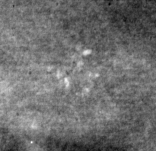
Region of interest cut from a scanned film mammogram (one marked finding); left breast; CC view.
Calcifications, morphology punctate, distribution clustered; BI-RADS assessment category 4; subtlety rating 1 on a 1 (subtle) to 5 (obvious) scale; pathology result (as recorded, not read from the image): malignant.